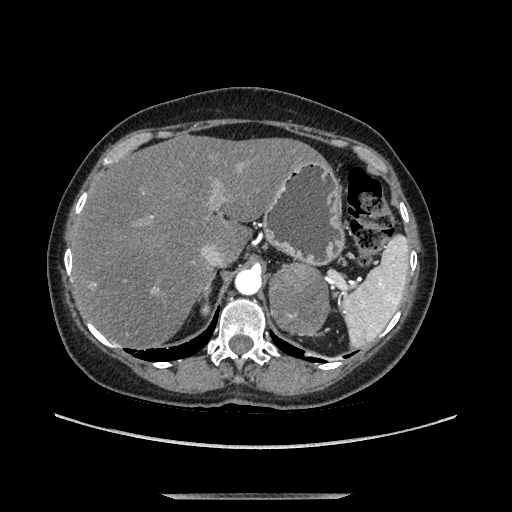
Contrast-enhanced abdominal CT, one axial slice; soft-tissue window (W 400 / L 40 HU); 1.25 mm slice thickness; 512 × 512 image matrix. Female patient. Case-level facts recorded for this patient, not image findings: diagnosis: adrenocortical carcinoma; tumour side: left adrenal; tumour size at pathology: 9 cm; Ki-67 index: 2 %; stage (as recorded): 3.
Outlined on this slice (semi-automatically segmented with operator editing):
- mass: bounding box (x1, y1, x2, y2) in pixels: (271, 265, 327, 332)